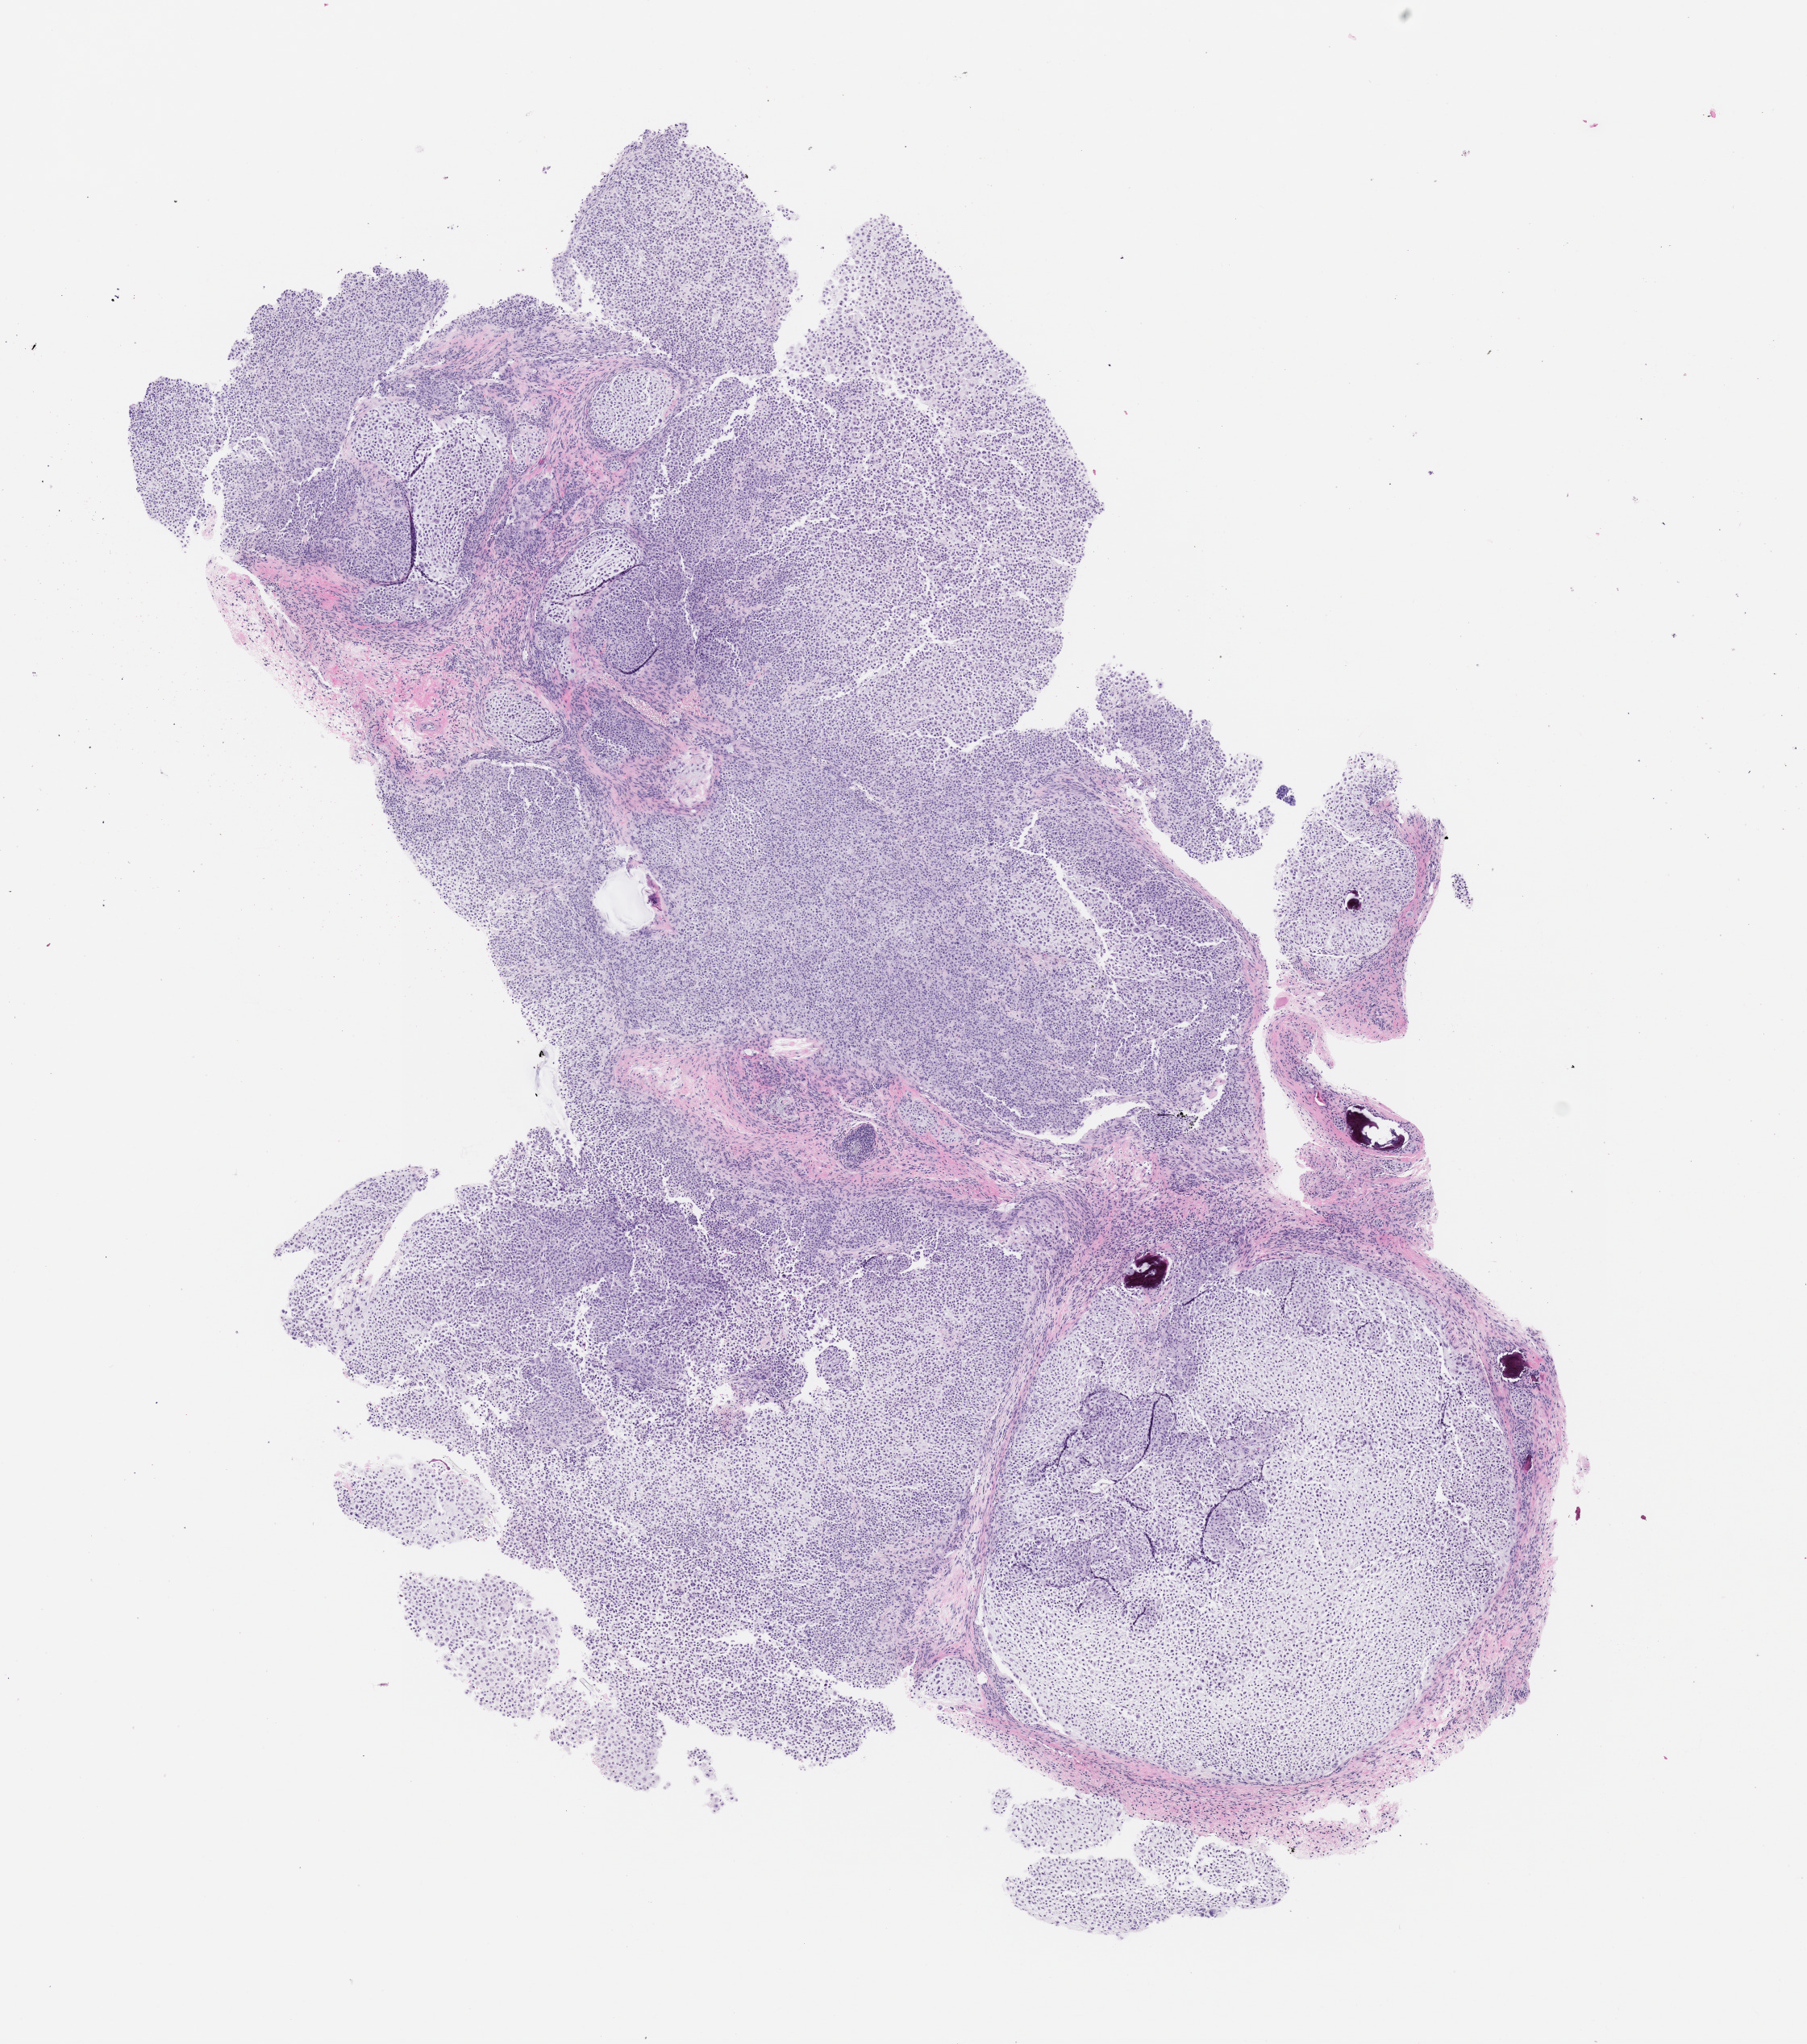
Whole-slide image, H&E: patient-derived xenograft (human tumor grown in a mouse), passage 2 — whole scanned area (about 9.0 x 10.2 mm) shown as a low-resolution overview. Formalin-fixed paraffin-embedded section. Tumor site category: musculoskeletal.
Originating patient diagnosis: Chondrosarcoma.